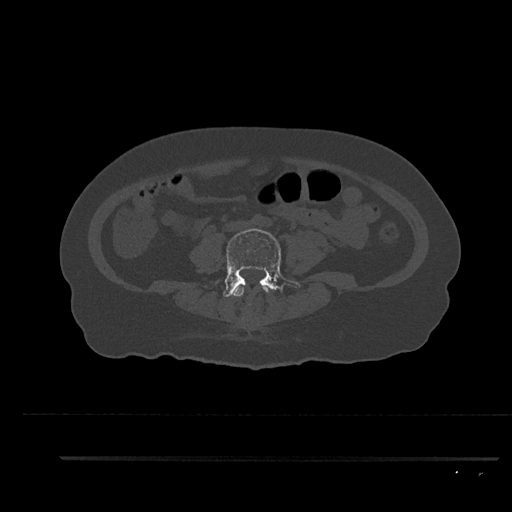
CT including the spine, one axial slice; position 35 of 797 along the scan axis; 120 kVp; bone window (W 1800 / L 400 HU); 0.5 mm slice thickness; 512 × 512 image matrix, field of view 408 × 408 mm. Female patient, age 44 years. Case-level facts recorded for this patient, not image findings: primary cancer: renal; vertebrae with lytic lesions (as recorded): L1.
Annotated regions visible in this slice (semi-automatically segmented with operator editing):
- L3 vertebra: bounding box [x1, y1, x2, y2] px = [232, 284, 271, 297]
- L4 vertebra: [223, 228, 300, 305]